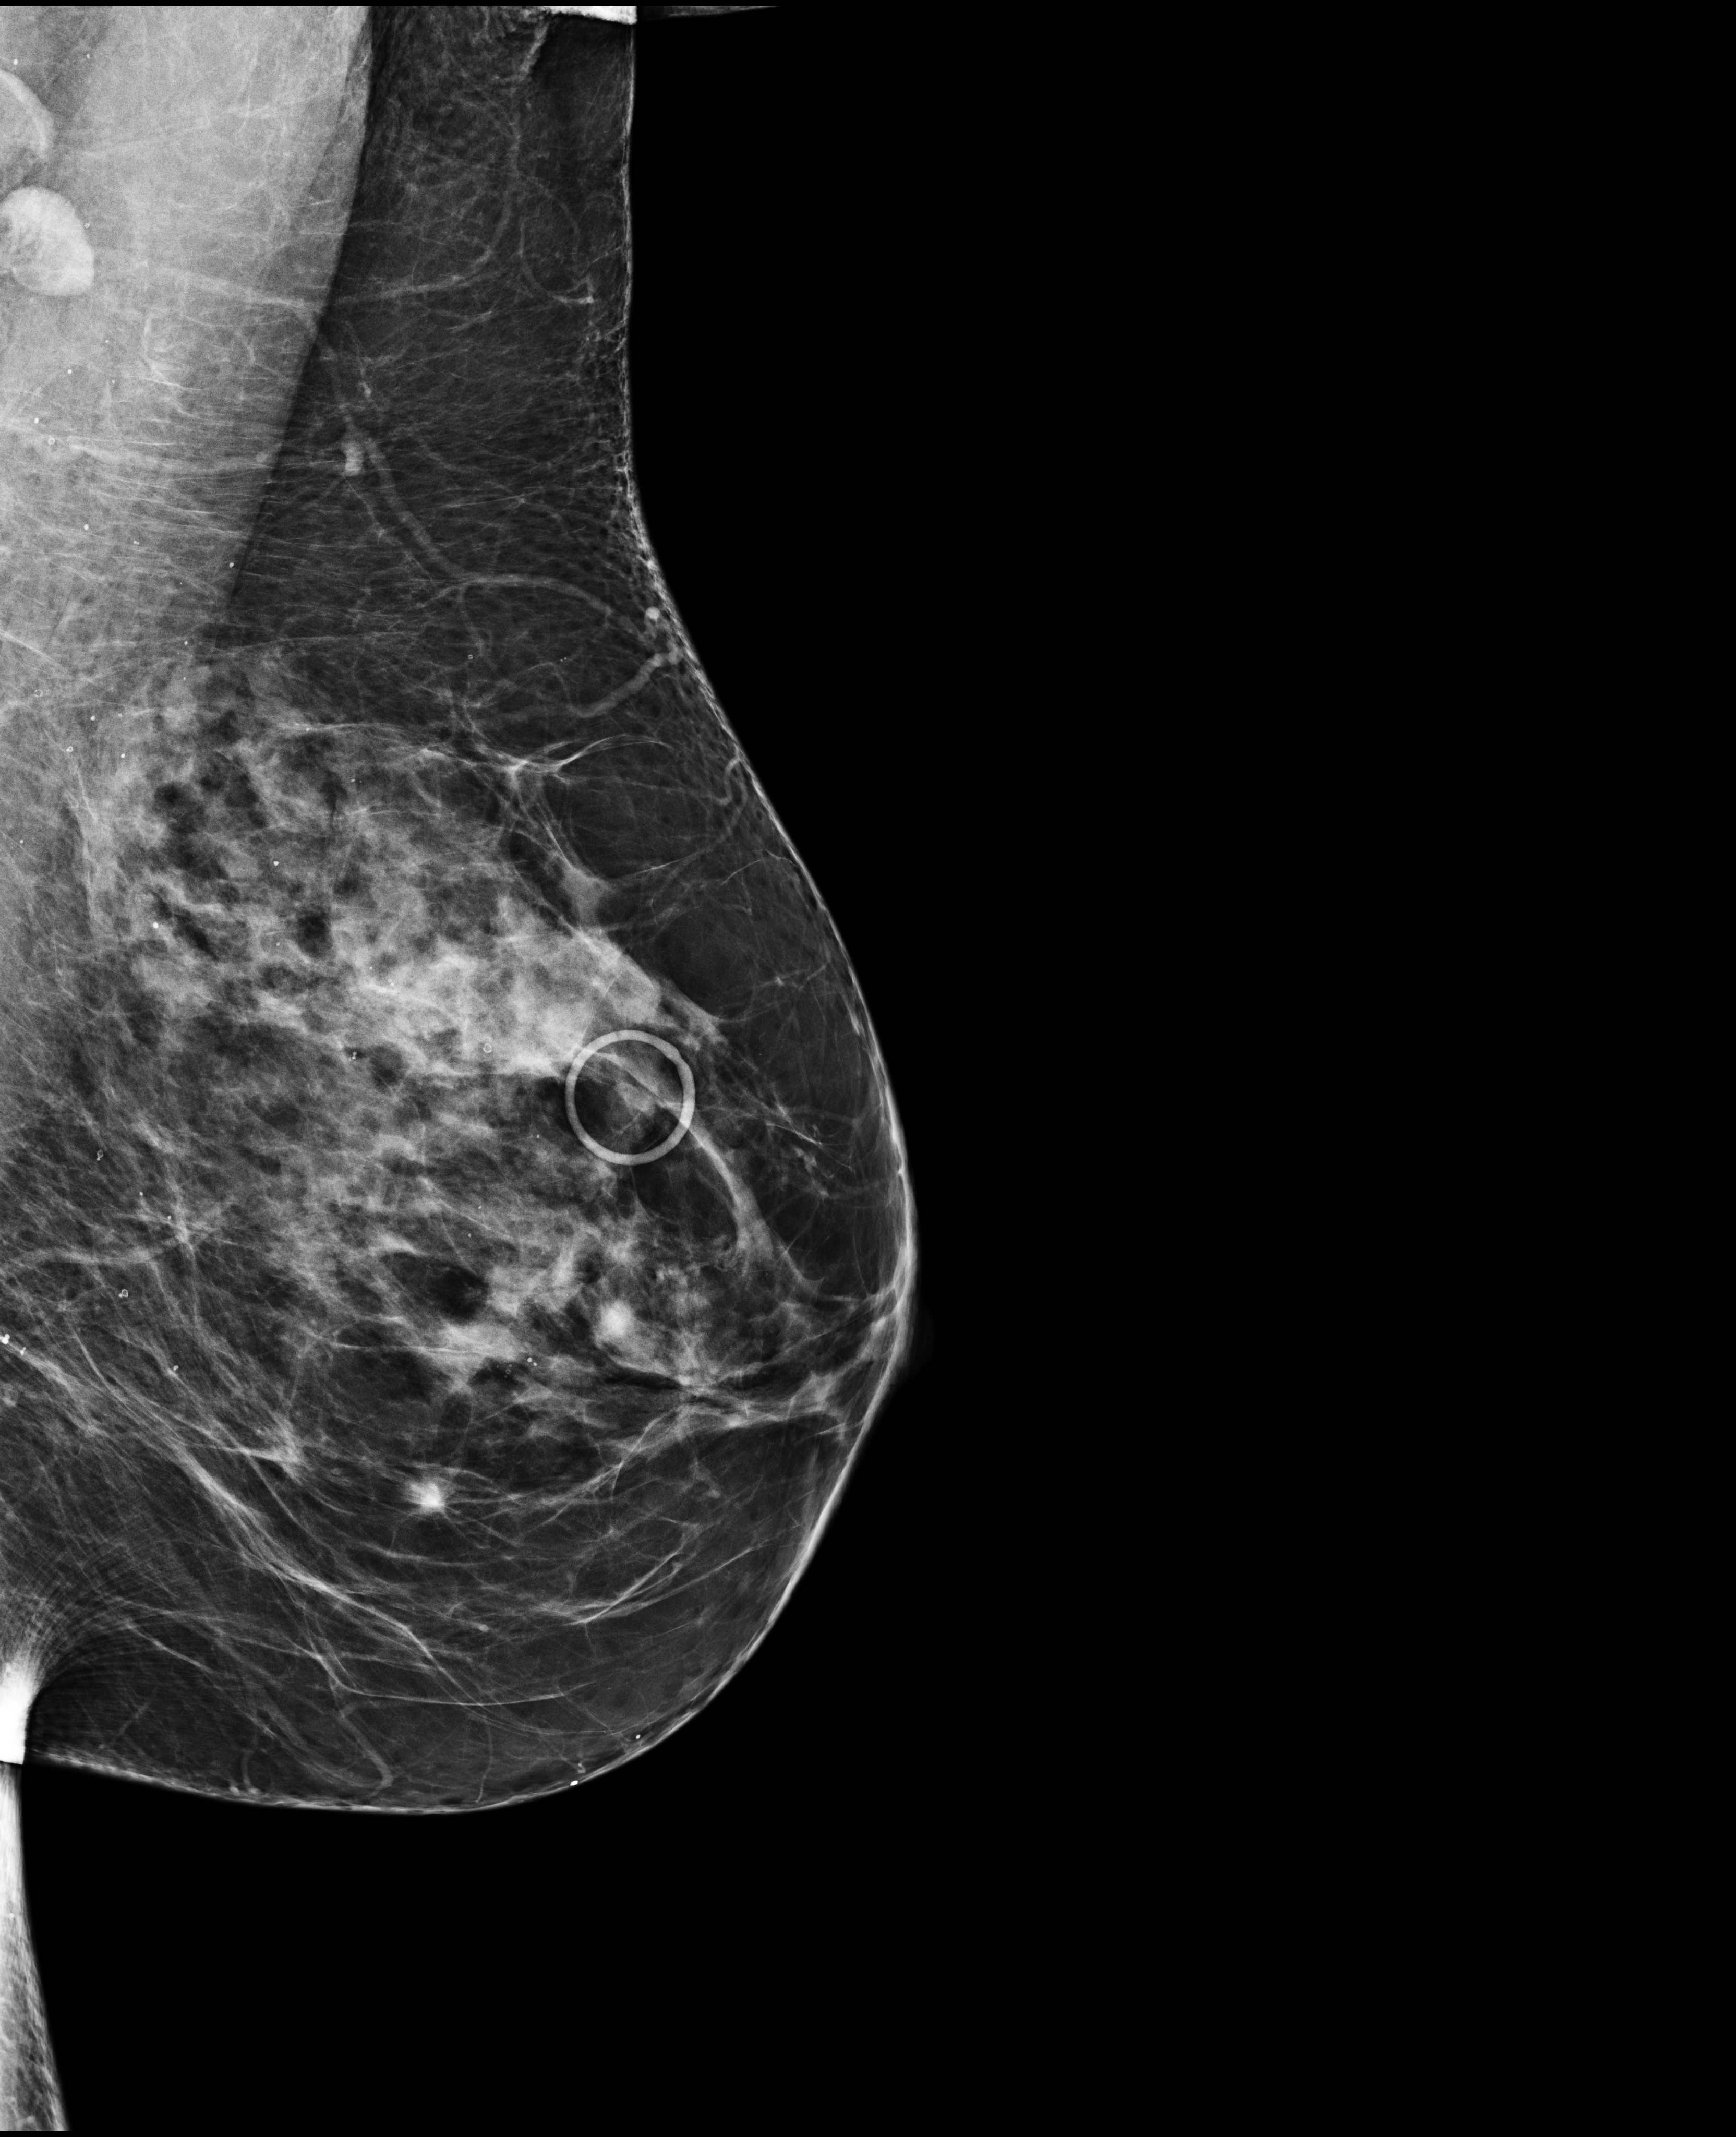
Full-field digital mammogram (FFDM), left breast, mediolateral oblique (MLO) view, annual screening mammography examination, compressed breast thickness 73 mm. Female patient, age 60 years.
Breast density at the screening exam (both breasts): heterogeneously dense (BI-RADS density category c). Final BI-RADS assessment for this screening round (tomosynthesis exam, both breasts): category 1. Recall: recalled for additional imaging after this screen.